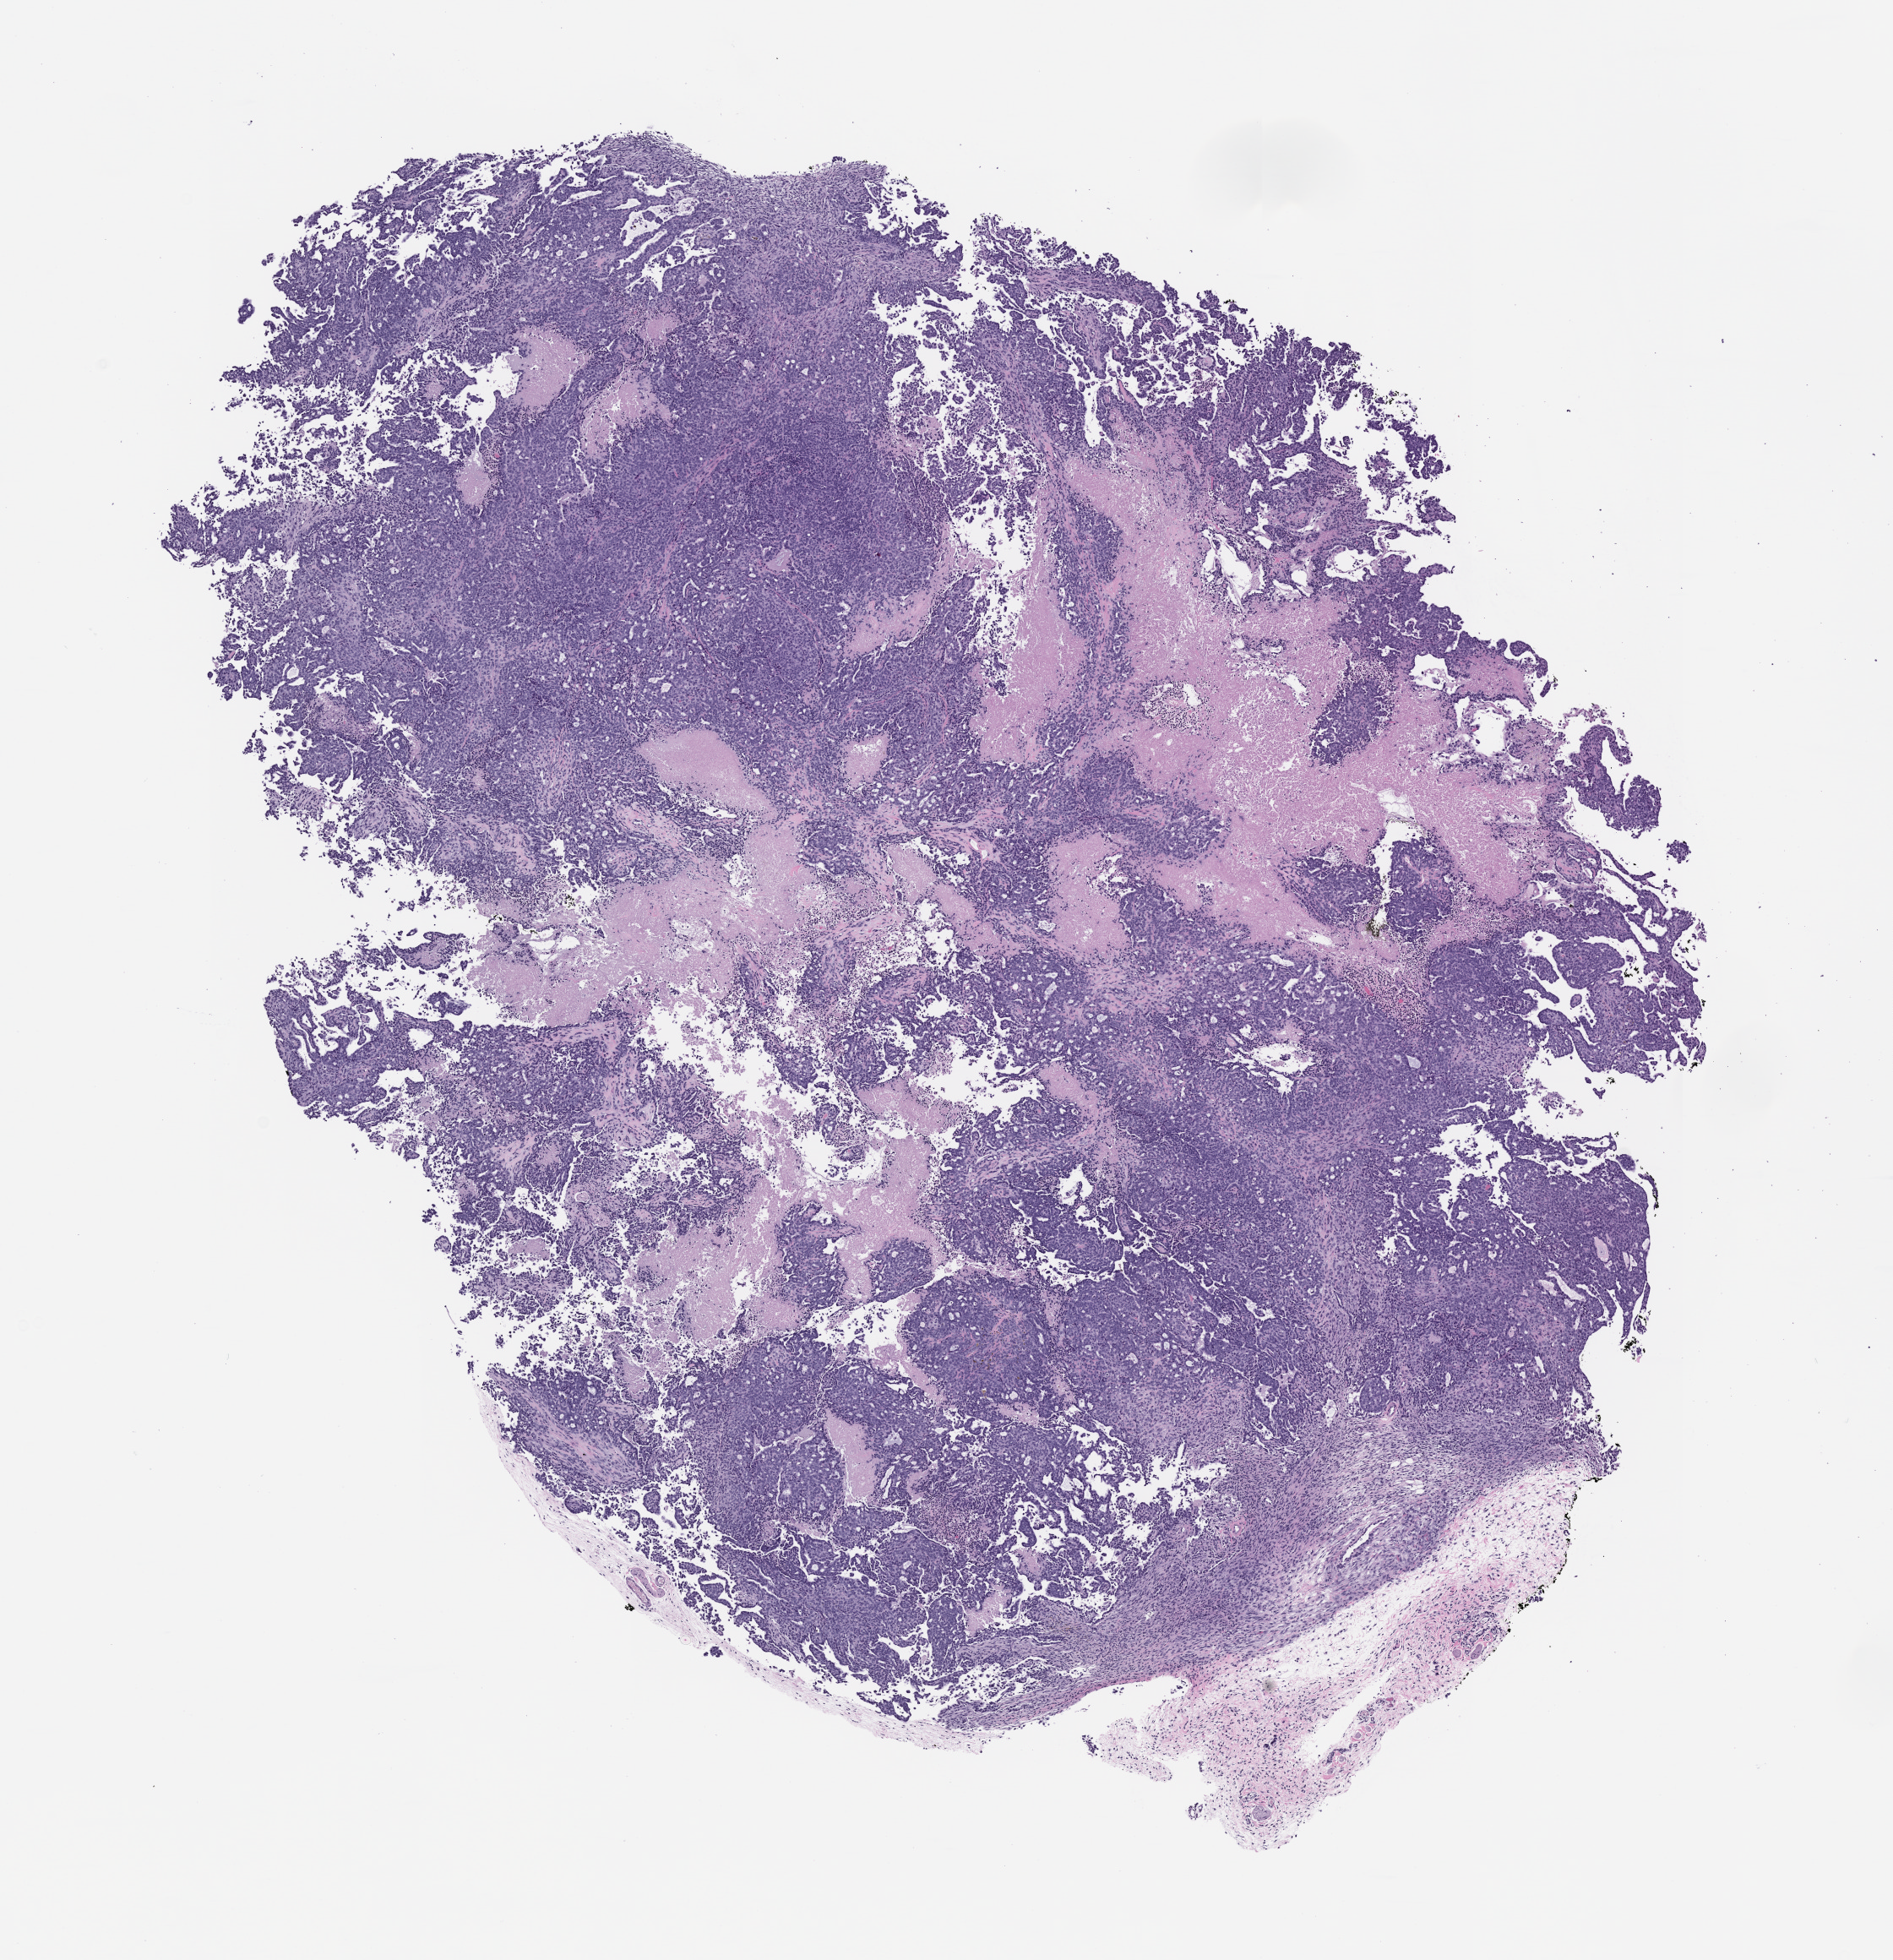
Whole-slide image, H&E: patient-derived xenograft (human tumor grown in a mouse), passage 1, low-resolution overview of the scanned area, about 9.0 x 9.3 mm, formalin-fixed paraffin-embedded section.
* originating patient diagnosis: Mesothelial Neoplasm